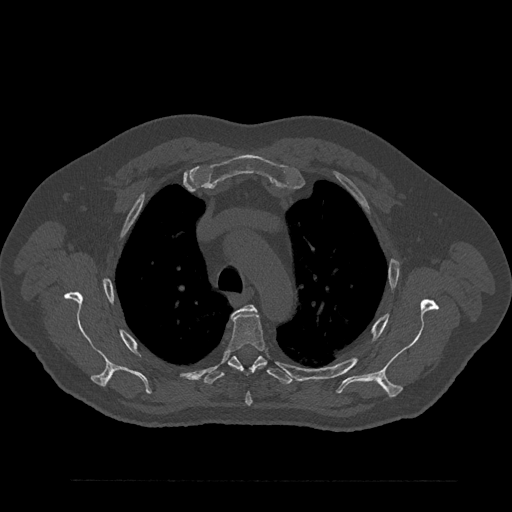
CT including the spine, one axial slice. Position 630 of 797 along the scan axis. Reconstruction kernel Br40s/3. 120 kVp. Bone window (W 1800 / L 400 HU). 0.5 mm slice thickness. 512 × 512 image matrix, field of view 430 × 430 mm. Patient: male, 61 years. From the clinical record (not read from this slice): primary cancer: prostate.
Annotated regions visible in this slice (semi-automatically segmented with operator editing):
- T3 vertebra: bounding box <238,305,256,312> (left, top, right, bottom; pixels)
- T4 vertebra: <227,310,266,406>
- T5 vertebra: <204,356,292,385>